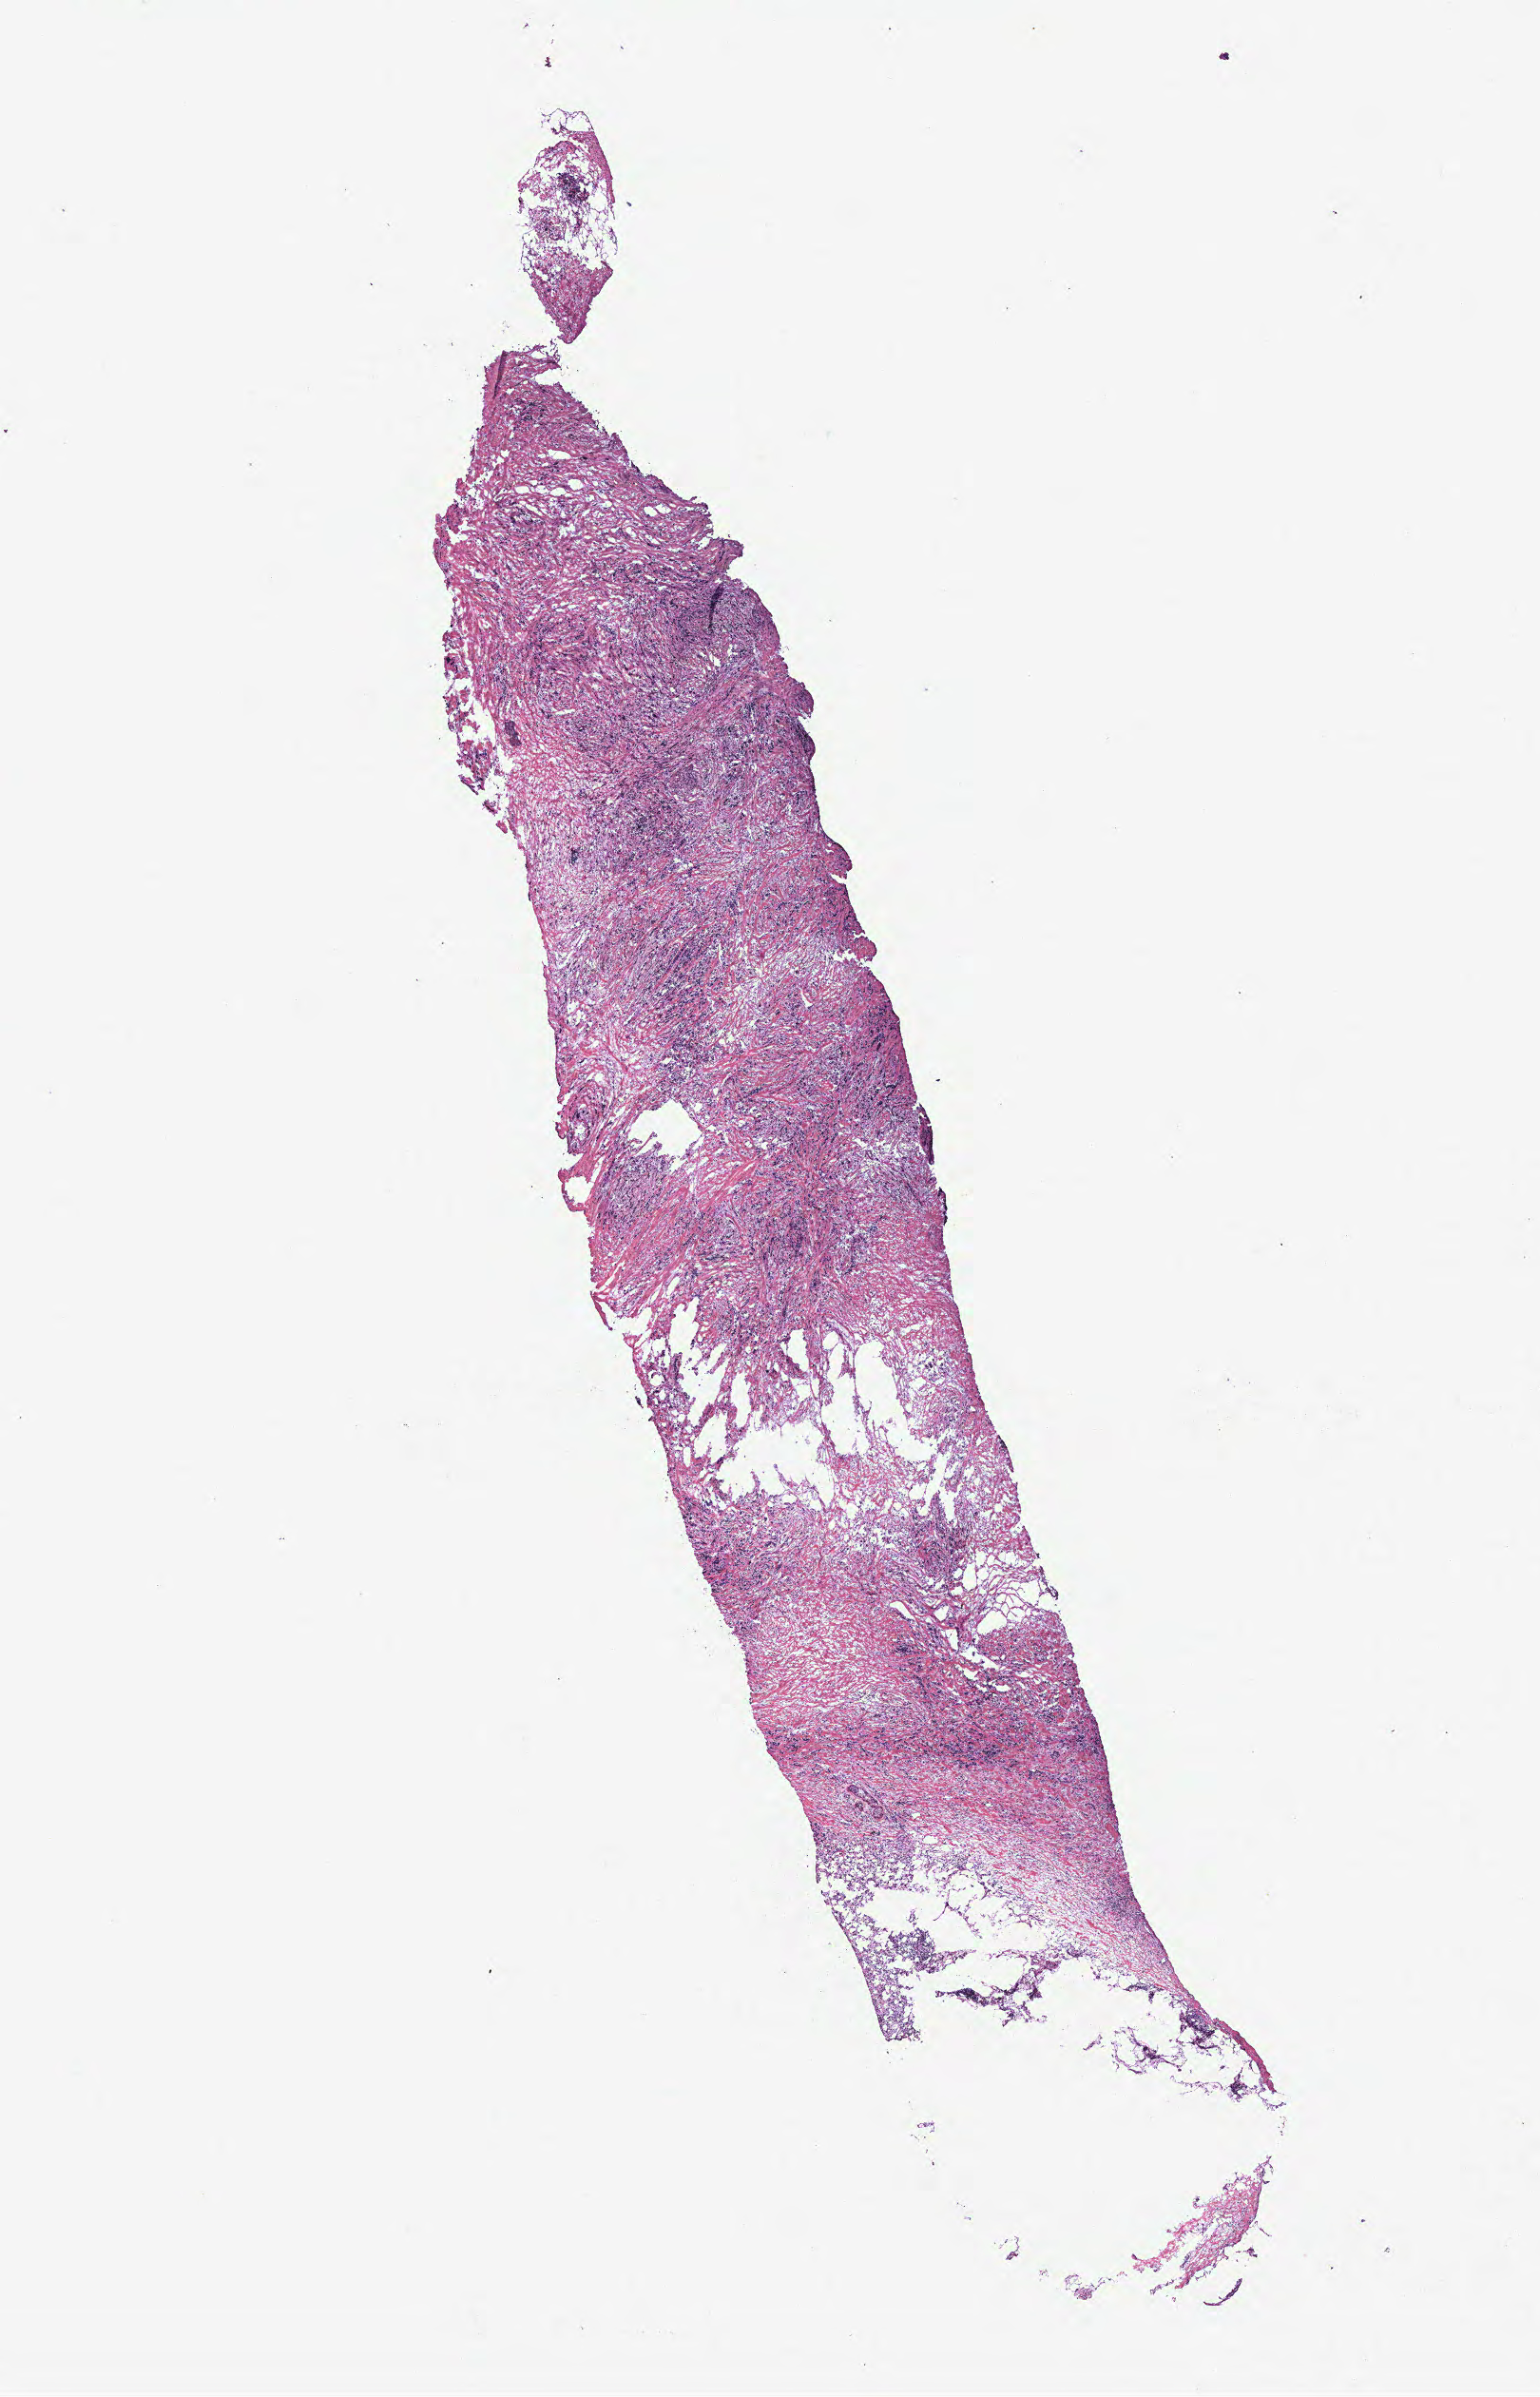
H&E whole-slide image — shown as a low-resolution overview of the whole scanned area (about 13.0 x 20.2 mm). Breast, tumour tissue. Patient: female, age 40 years.
• AJCC pathologic stage: III
• histologic diagnosis: Infiltrating lobular carcinoma, NOS